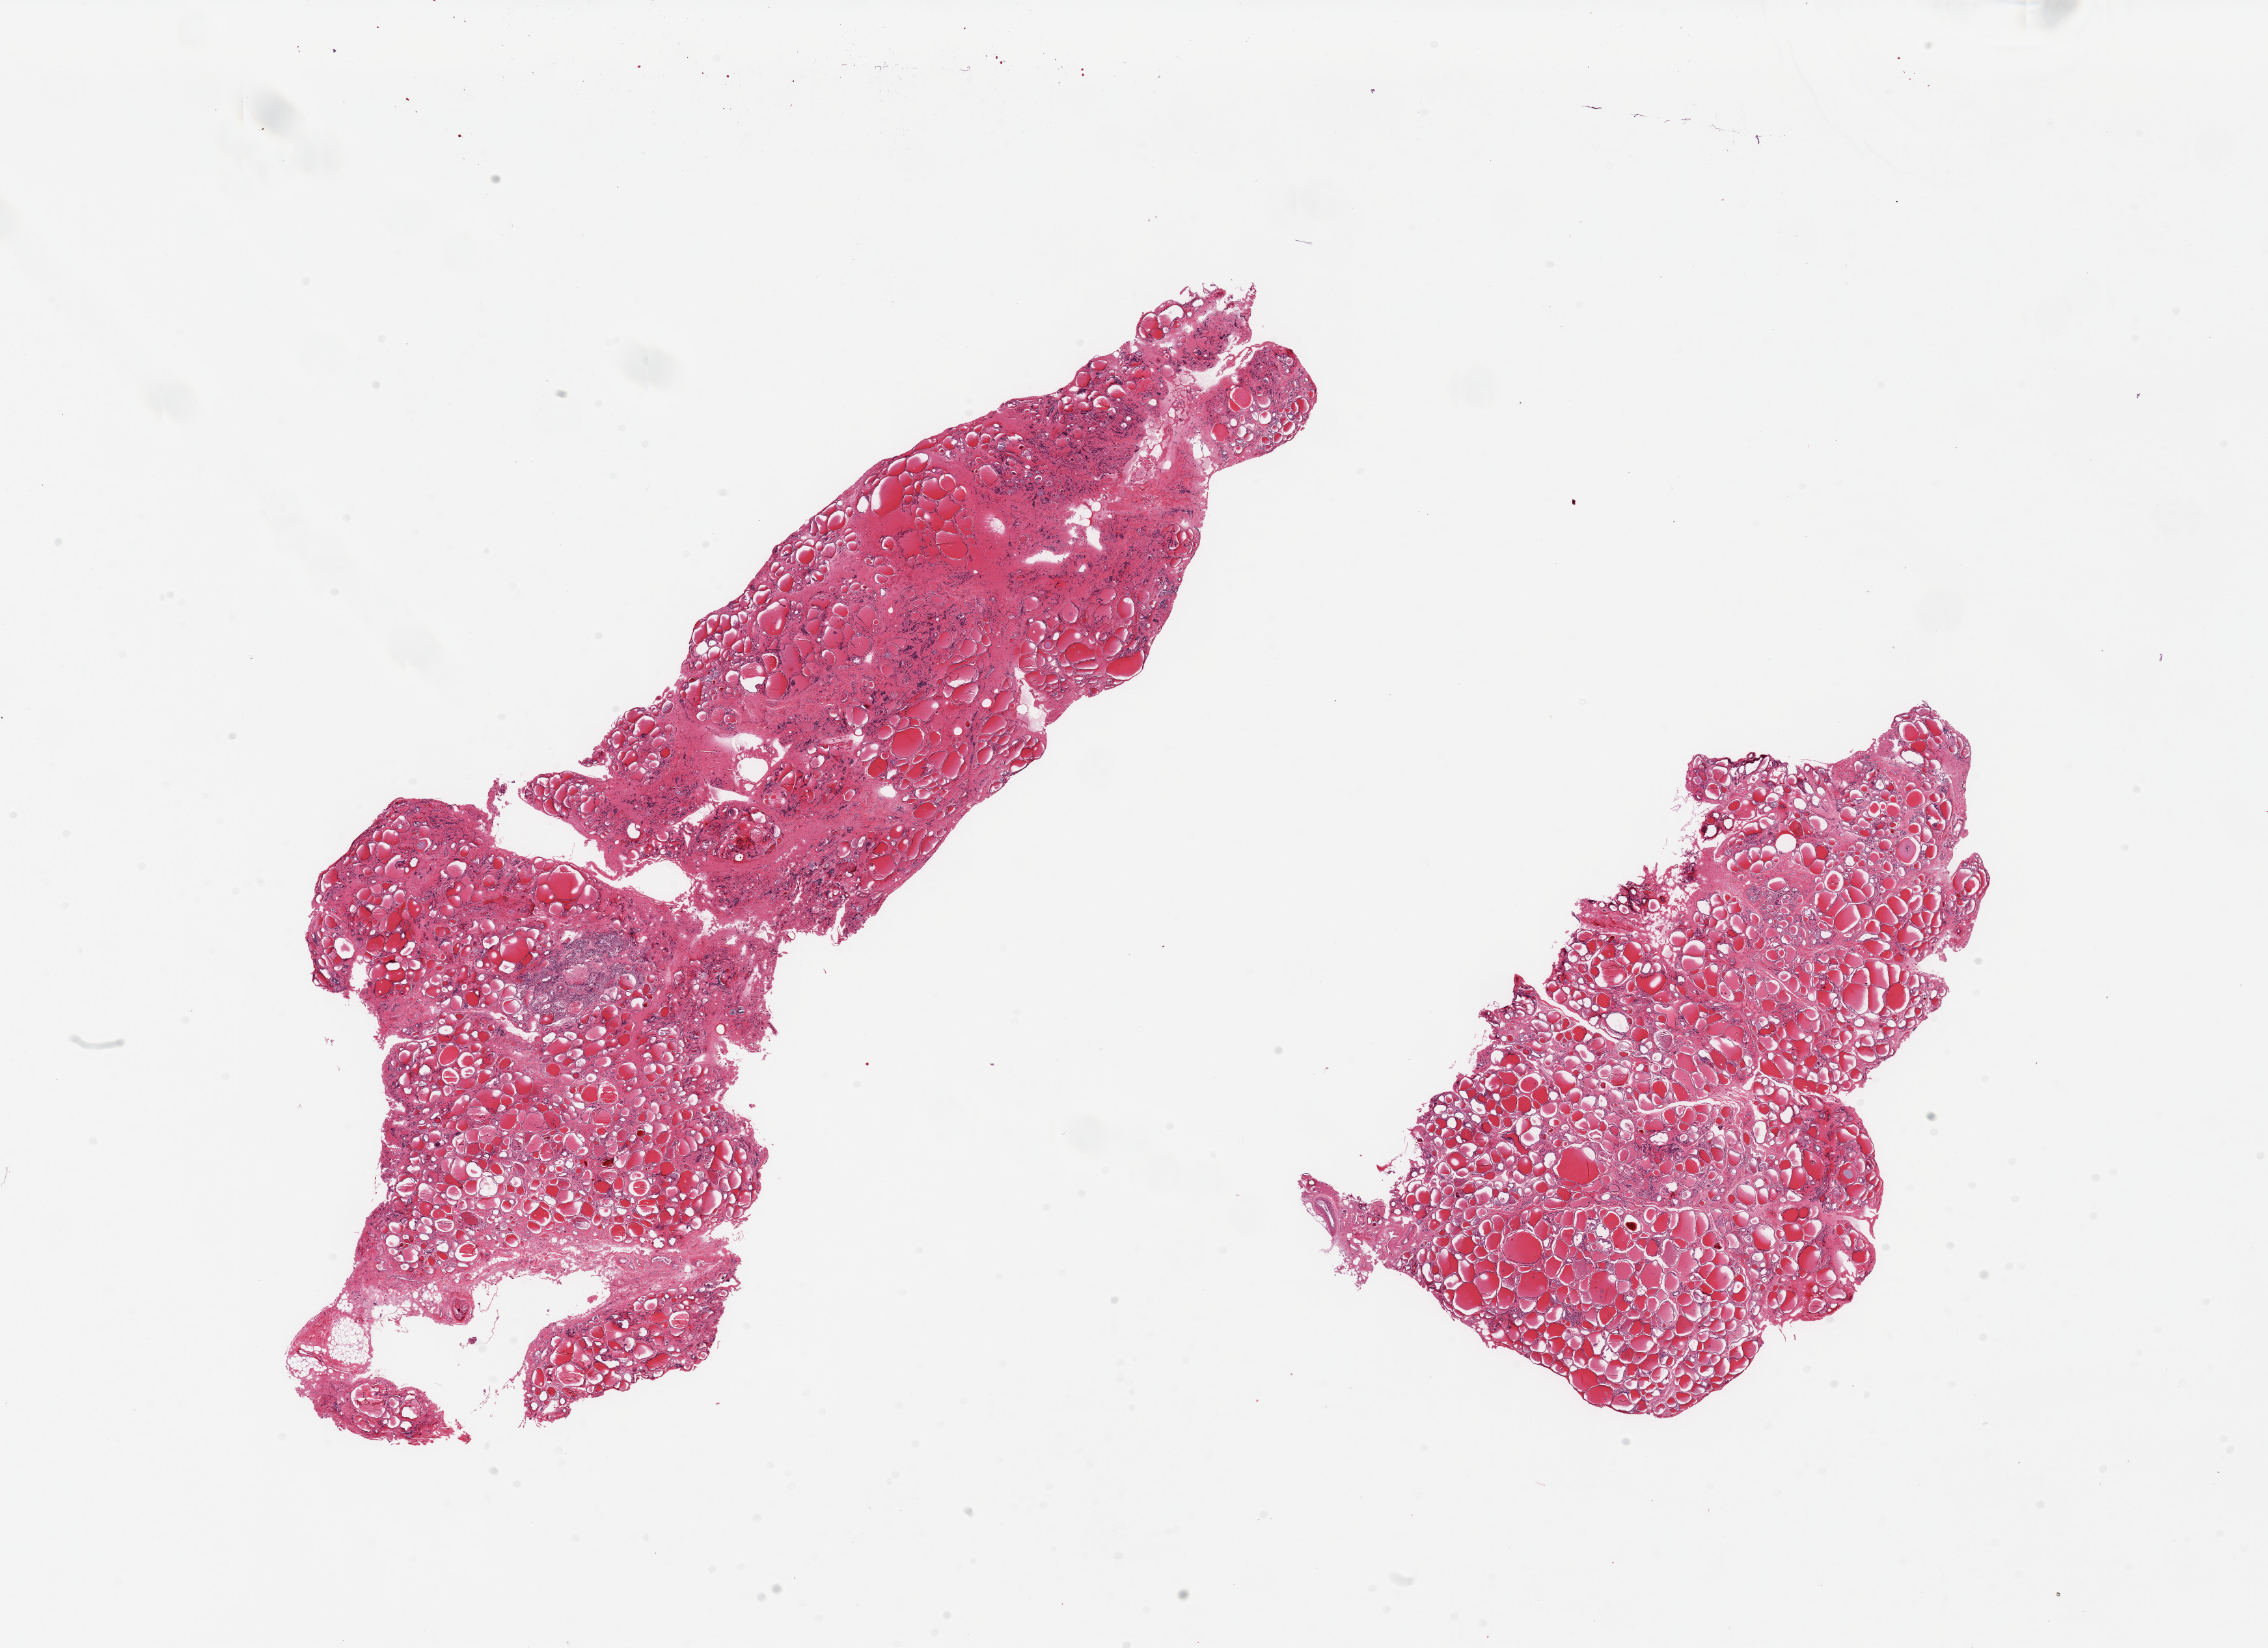
Hematoxylin and eosin (H&E) whole-slide image, brightfield, a low-resolution overview of the entire scanned area, about 27.6 x 20.0 mm (acquisition: 20x scan); PAXgene-fixed, paraffin-embedded tissue; target tissue: thyroid; tissue donor sample. Donor: male.
Pathologist's review note for this sample: 2 pieces; focus of gland disruption wiith lymphoid cells and small foci of fibrosis.